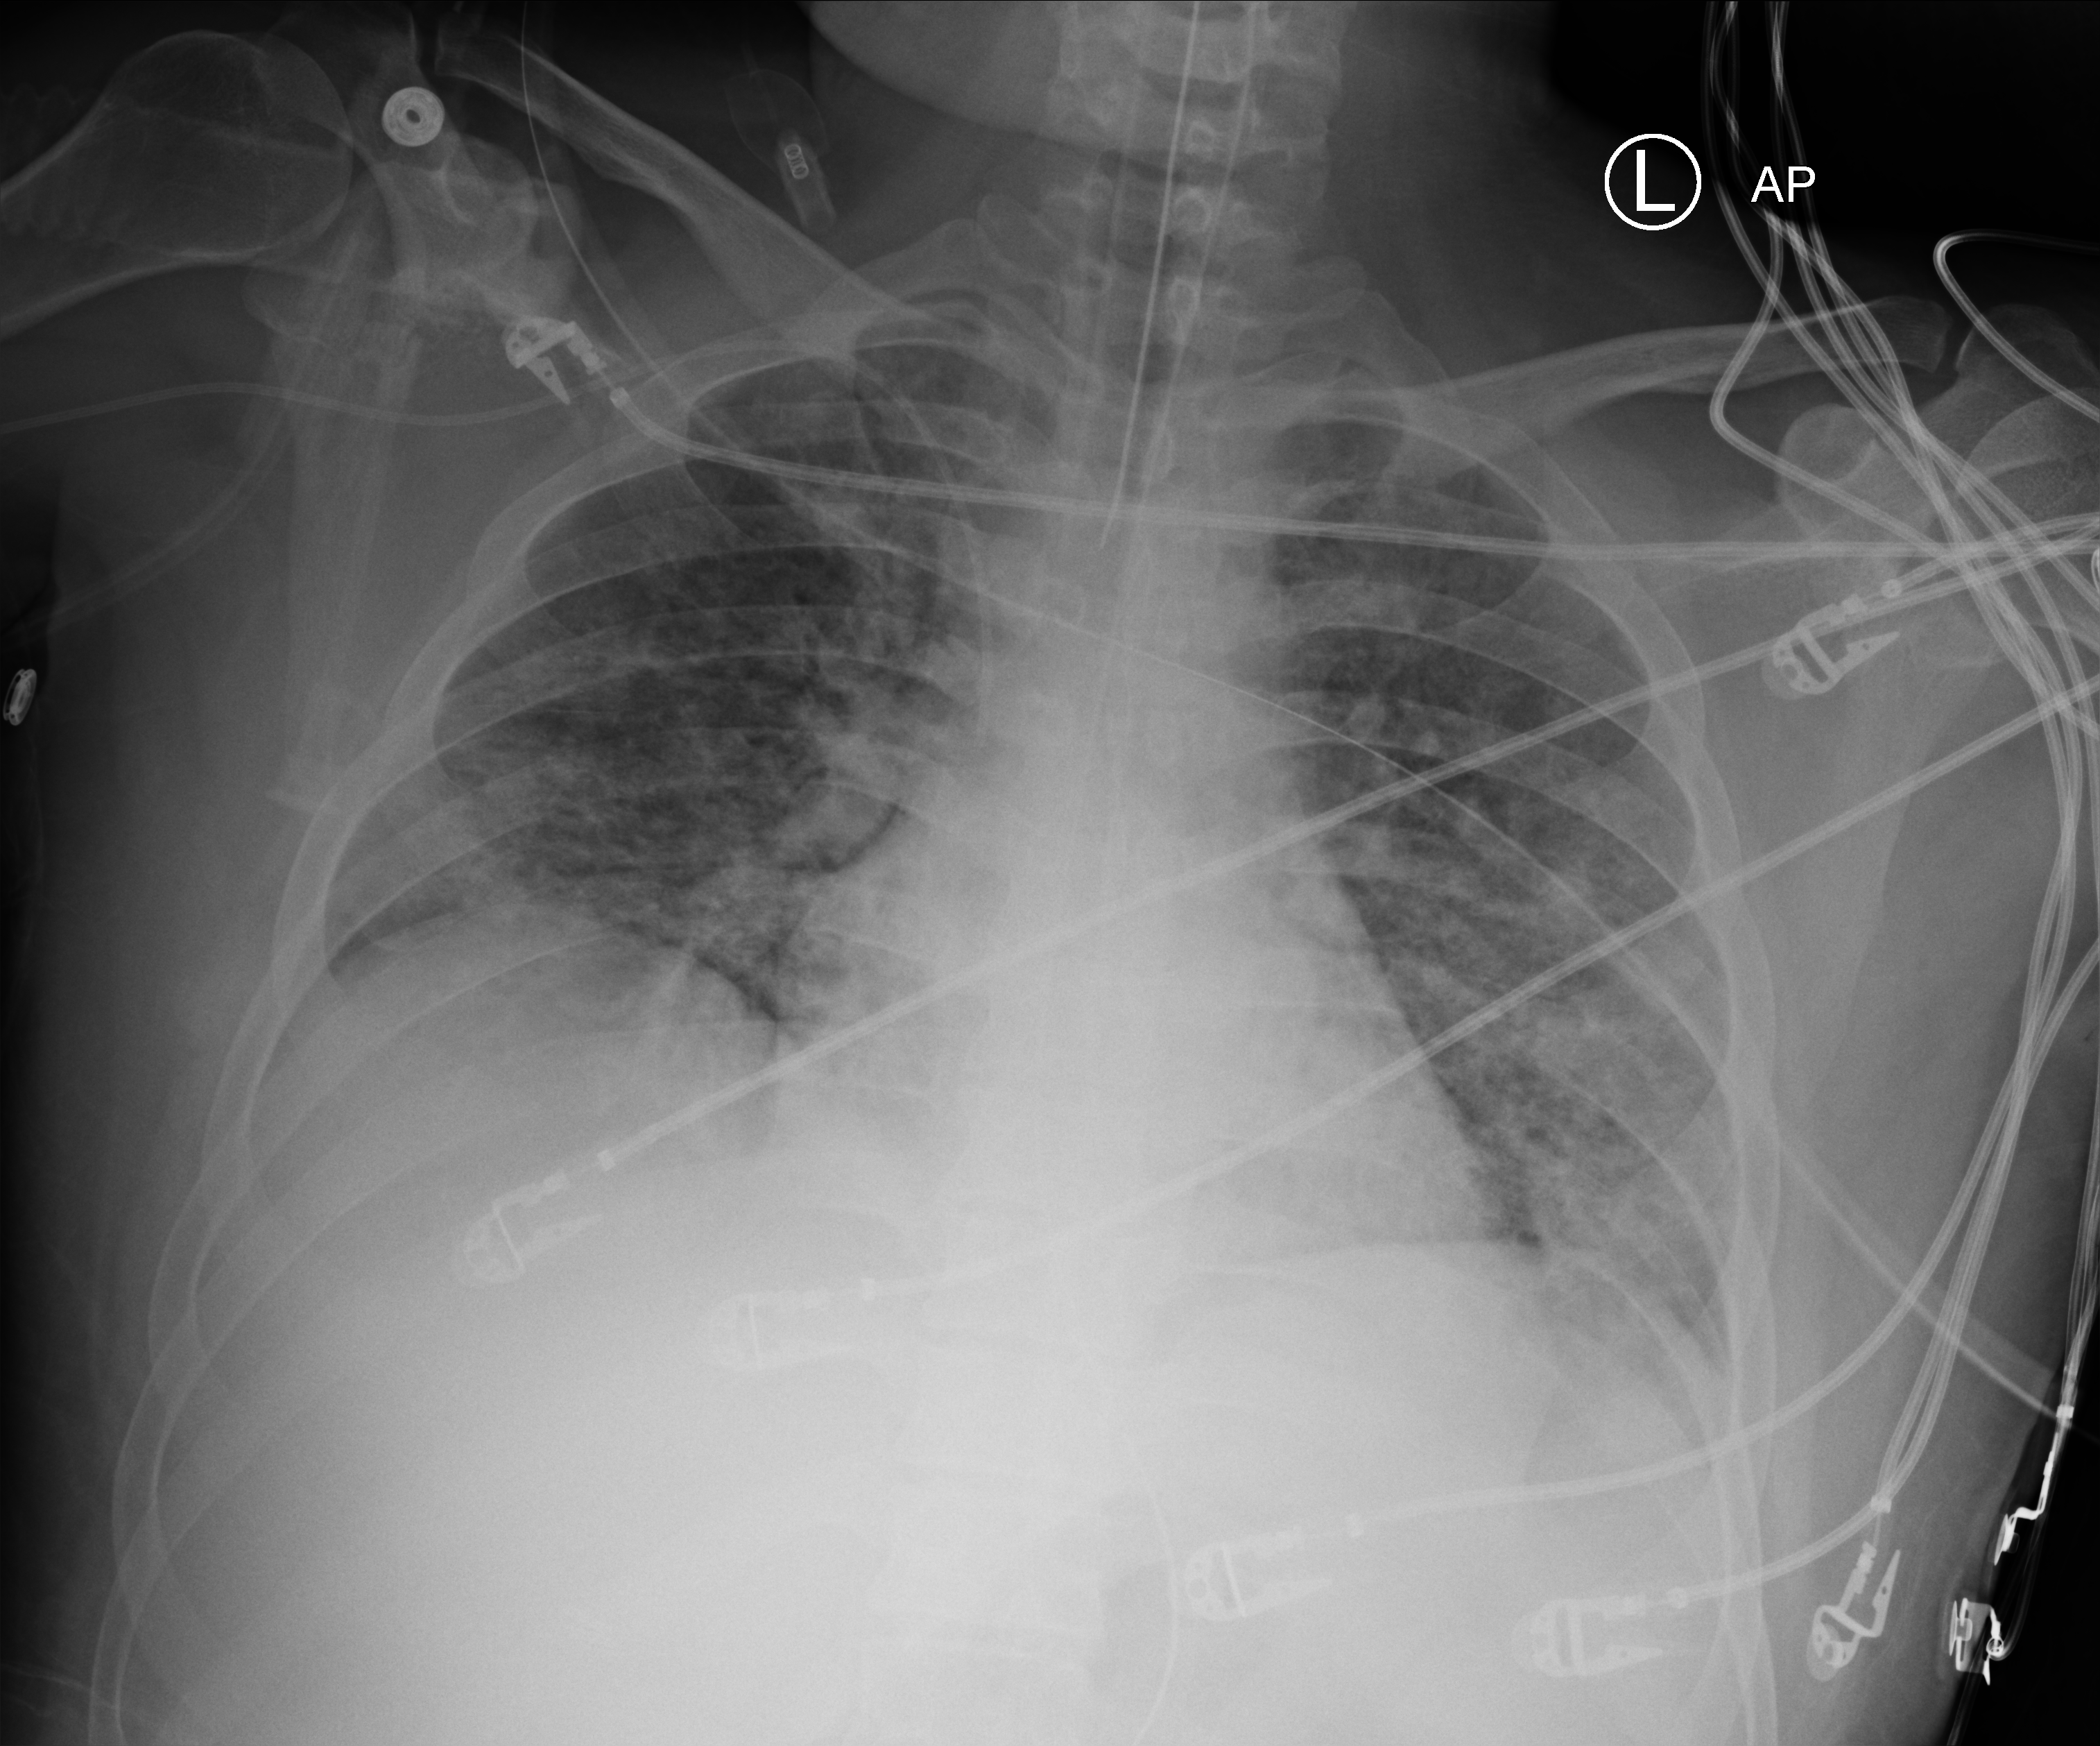
Portable chest radiograph; anteroposterior (AP) projection. Male patient hospitalised with COVID-19, age 18–59 years.
From the hospital-stay record, not from the radiograph (when in the stay this image was taken is not recorded): admitted to intensive care during this hospital stay: yes; COPD (admission record): no; mechanically ventilated during this hospital stay: yes.